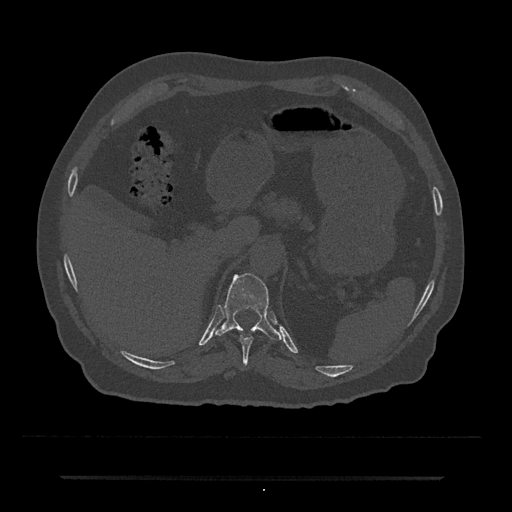
CT including the spine, one axial slice; slice 194 of 797 in the series (ordered by position); reconstruction kernel Br40s/3; bone window (W 1800 / L 400 HU); 0.5 mm slice thickness; 512 × 512 image matrix. Male patient, age 69 years. From the clinical record (not read from this slice): primary cancer: prostate.
Structures marked on this image (semi-automatic segmentation, software-assisted and operator-edited):
- T10 vertebra: bounding box (x1, y1, x2, y2) in pixels: (239, 336, 254, 364)
- T11 vertebra: (214, 273, 282, 341)